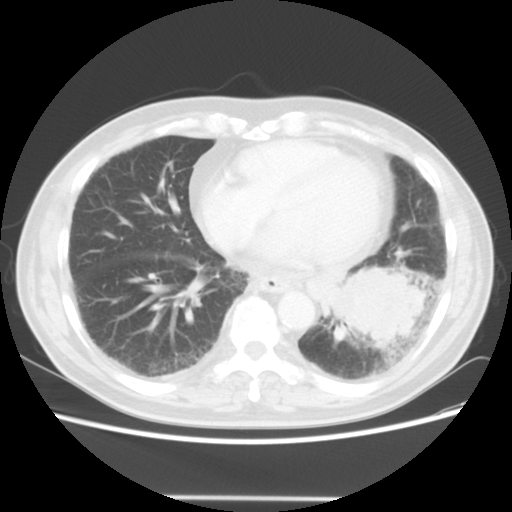
Chest CT, one axial slice. Position 17 of 56 along the scan axis. Reconstruction kernel STANDARD. 140 kVp. Lung window (W 1500 / L -600 HU). 5 mm slice thickness. 512 × 512 image matrix, field of view 360 × 360 mm. Male patient, age 66 years. Case-level facts recorded for this patient, not image findings: clinical TNM (as recorded): T4 N3 M0; histopathological grade: G3.
Annotated regions visible in this slice (rectangle marked by the reading radiologist):
- lung tumour (recorded histology: small cell carcinoma): box from (x=322, y=267) to (x=430, y=356) px